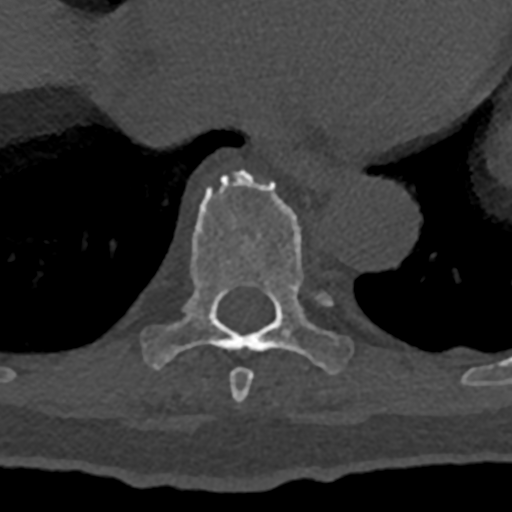
CT including the spine, one axial slice; position 662 of 797 along the scan axis; bone window (W 1800 / L 400 HU); 512 × 512 image matrix, field of view 160 × 160 mm. Patient: male, 74 years. From the clinical record (not read from this slice): primary cancer: renal; vertebrae with lytic lesions (as recorded): T10, L1, L2, L3, L4, L5.
Outlined on this slice (semi-automatically segmented with operator editing):
- T8 vertebra: bounding box (x1, y1, x2, y2) in pixels: (229, 368, 254, 402)
- T9 vertebra: (142, 170, 353, 374)